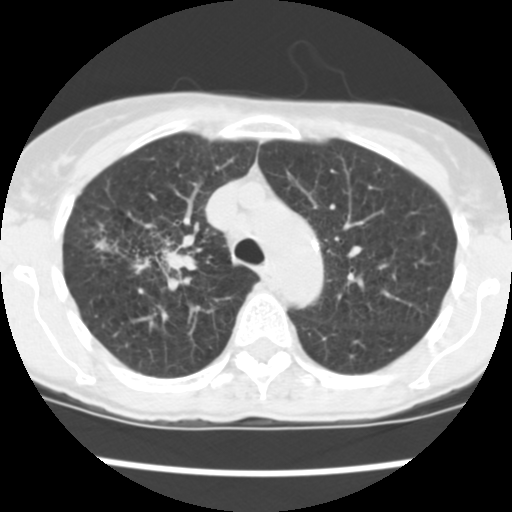
Low-dose screening chest CT, axial slice, first (baseline) screen, lung window (W 1500 / L -600 HU), standard (soft-tissue) reconstruction kernel (STANDARD), 512 × 512 image matrix, field of view 276 × 276 mm. Female participant, aged 60 years at enrolment. Current smoker at enrolment.
- Expert-annotated lung lesion, box from (x=84, y=215) to (x=203, y=286) px.
- The screening reader recorded 3 non-calcified nodules or masses ≥4 mm on this exam (right upper lobe, right upper lobe, right lower lobe); which of them this box marks is not recorded.
- Official screen result: positive, change unspecified: nodule(s) >= 4 mm or enlarging nodule(s), mass(es), or other non-specific abnormalities suspicious for lung cancer.